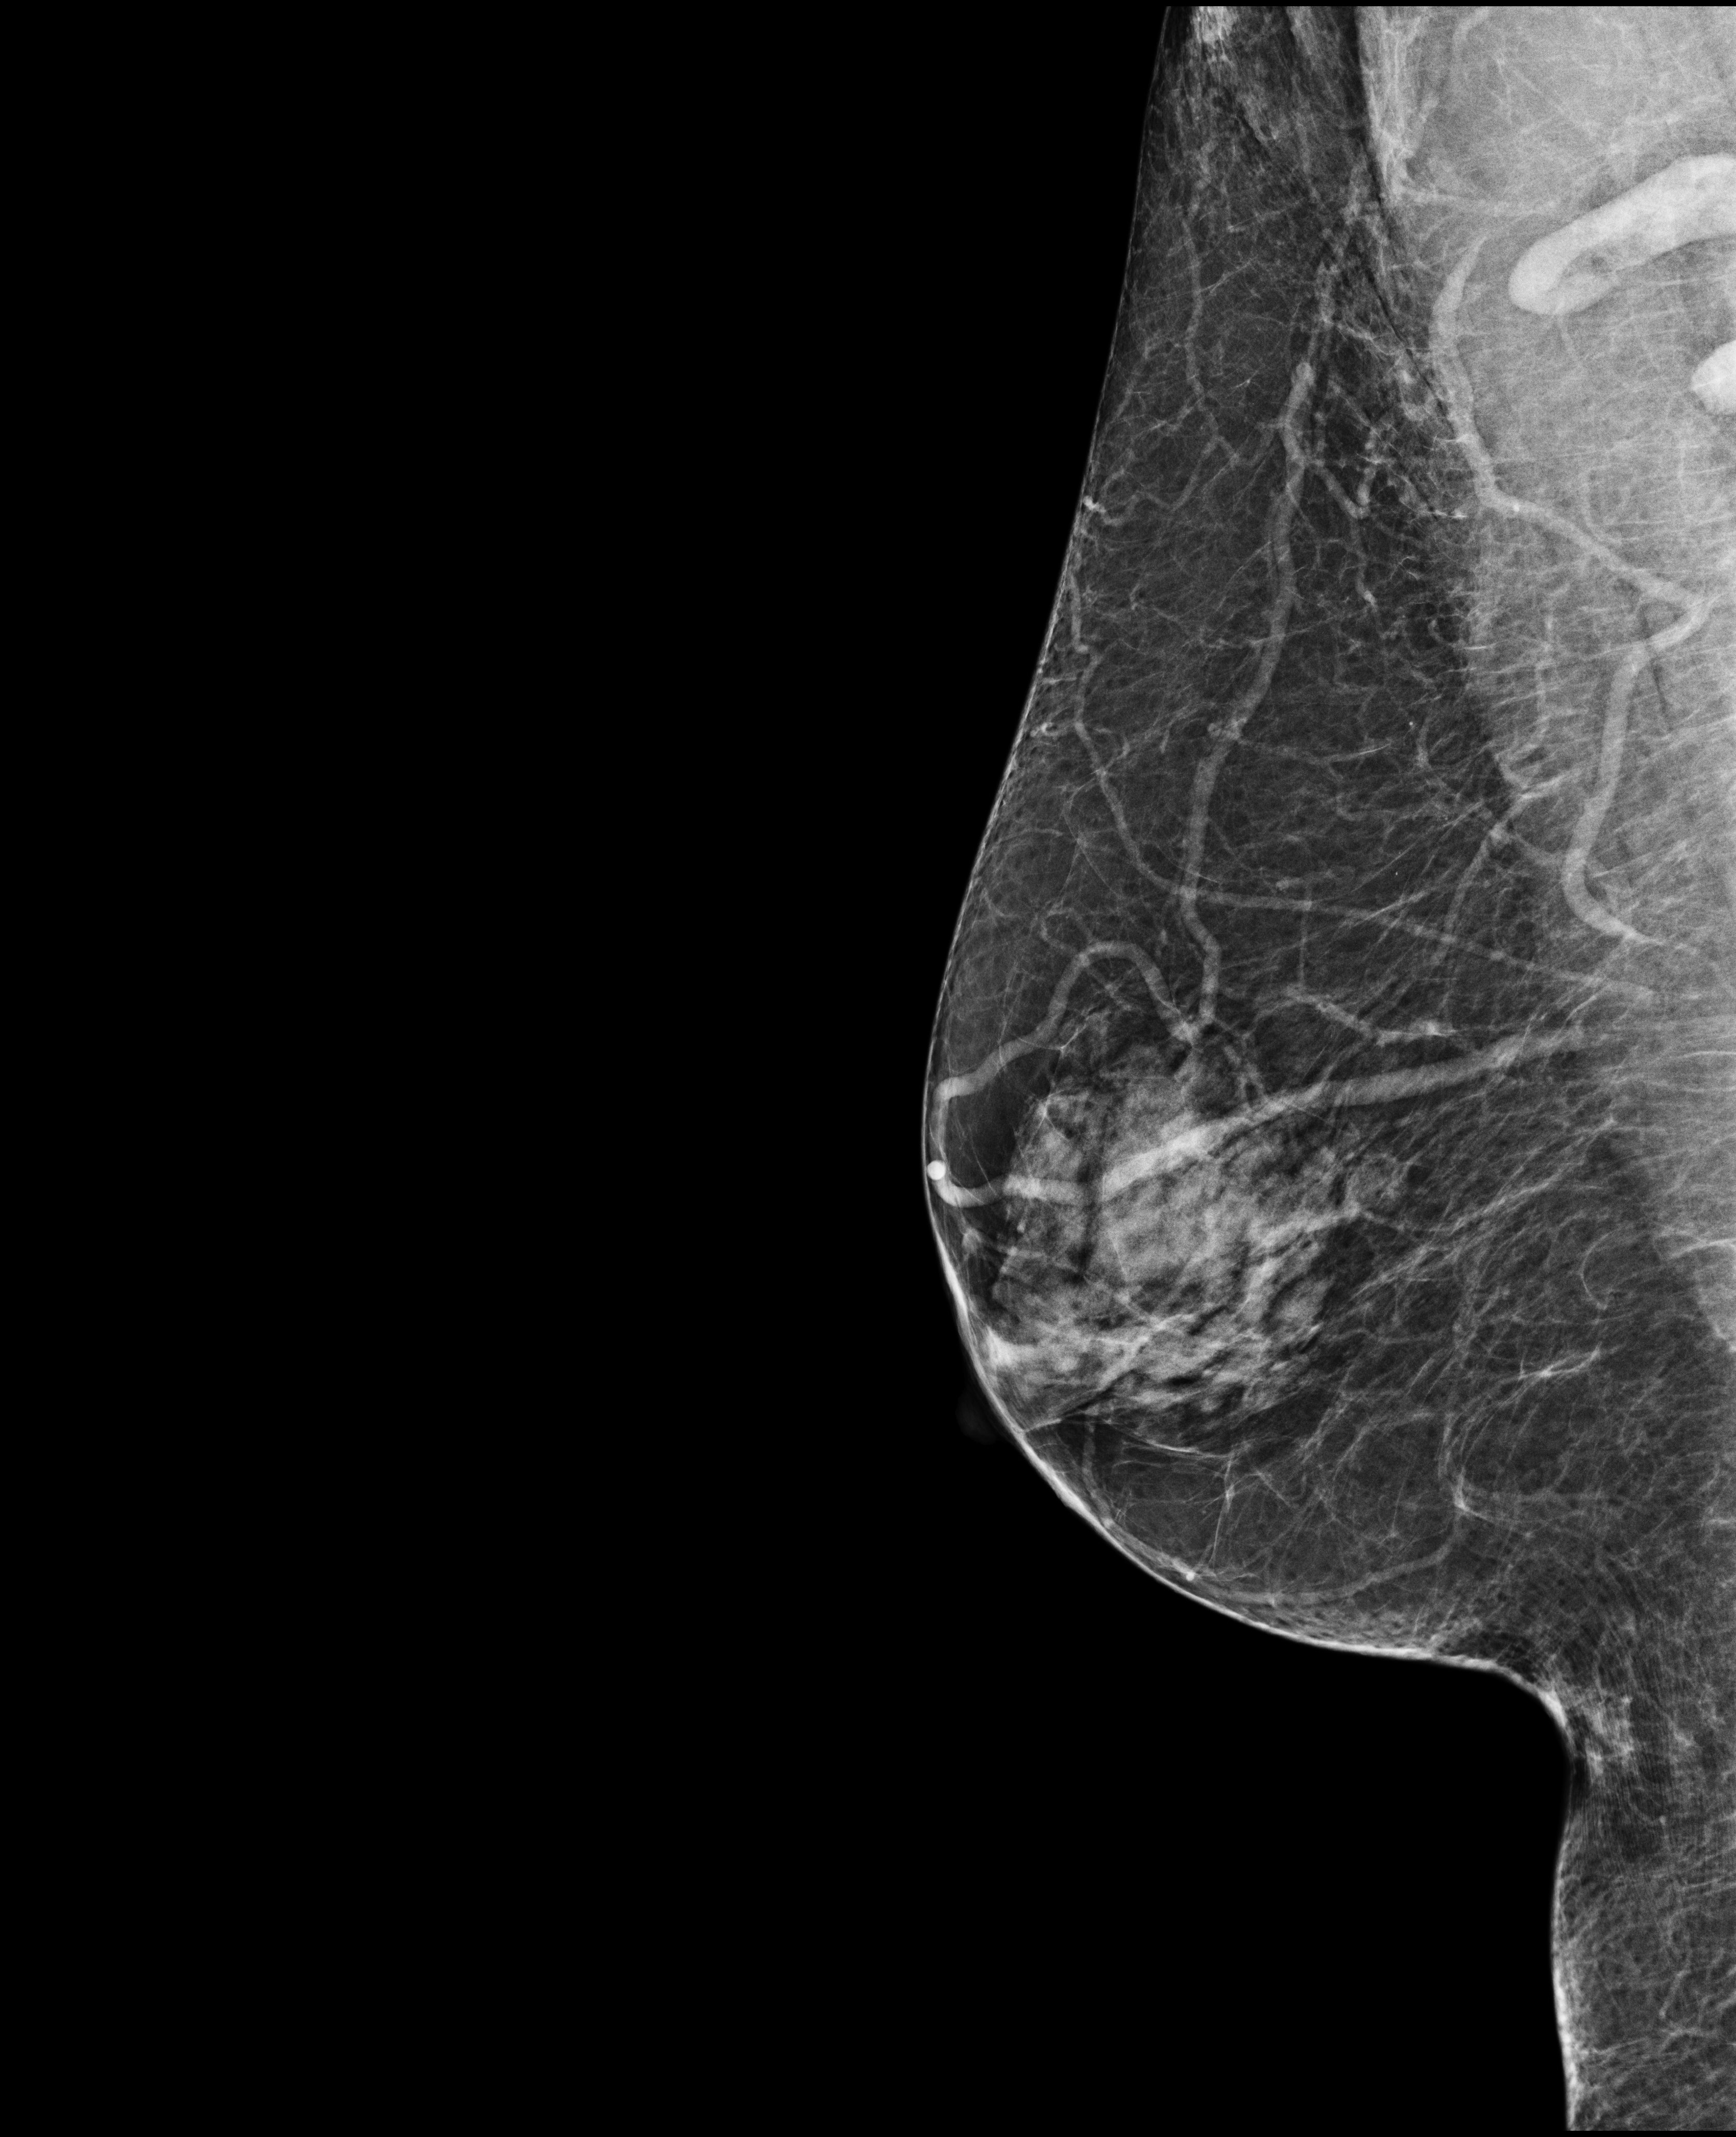
Screening examination.
Image type: full-field digital mammogram. Breast: right. Projection: mediolateral oblique (MLO) view.